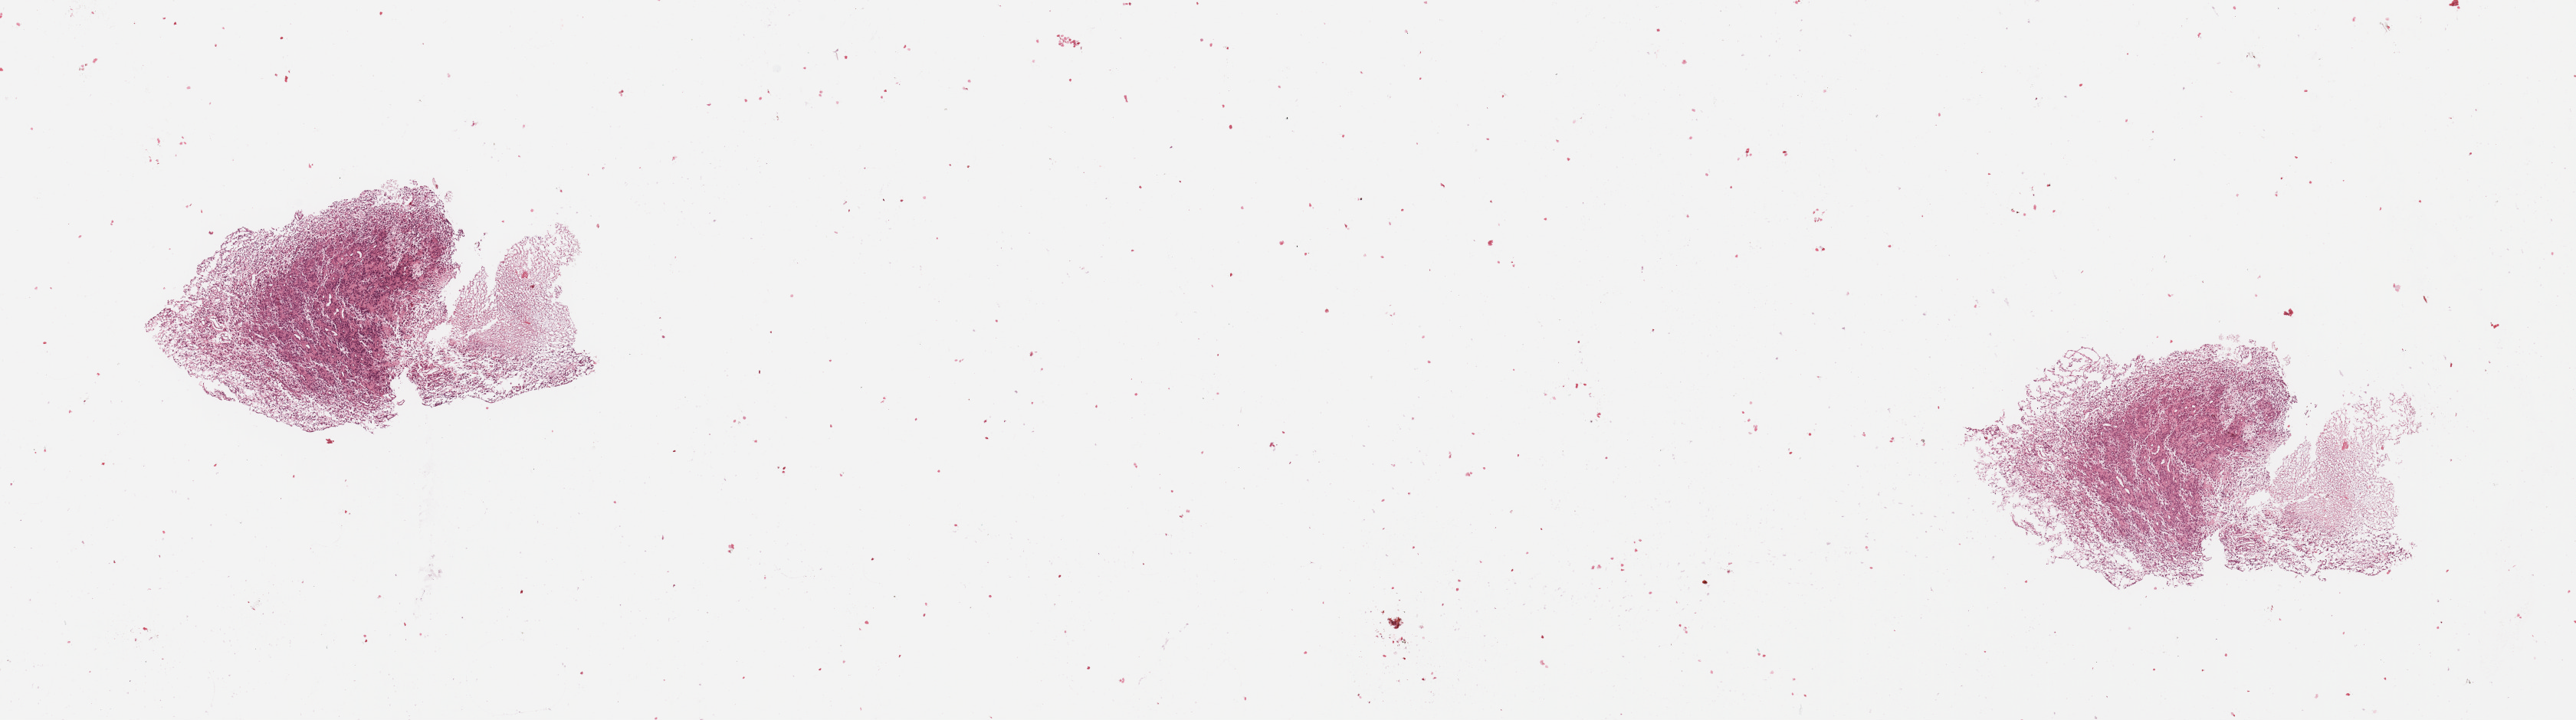
Digitized H&E-stained tissue section (whole slide) — low-resolution overview of the scanned area, about 26.6 x 7.4 mm. Tumour tissue sample, sampled site: brain. 74-year-old male patient. Pathologist review of this section (percent, as recorded): tumour nuclei 70%, necrosis 20%.
Primary tumour site (as recorded): temporal lobe. Diagnosis: Glioblastoma.